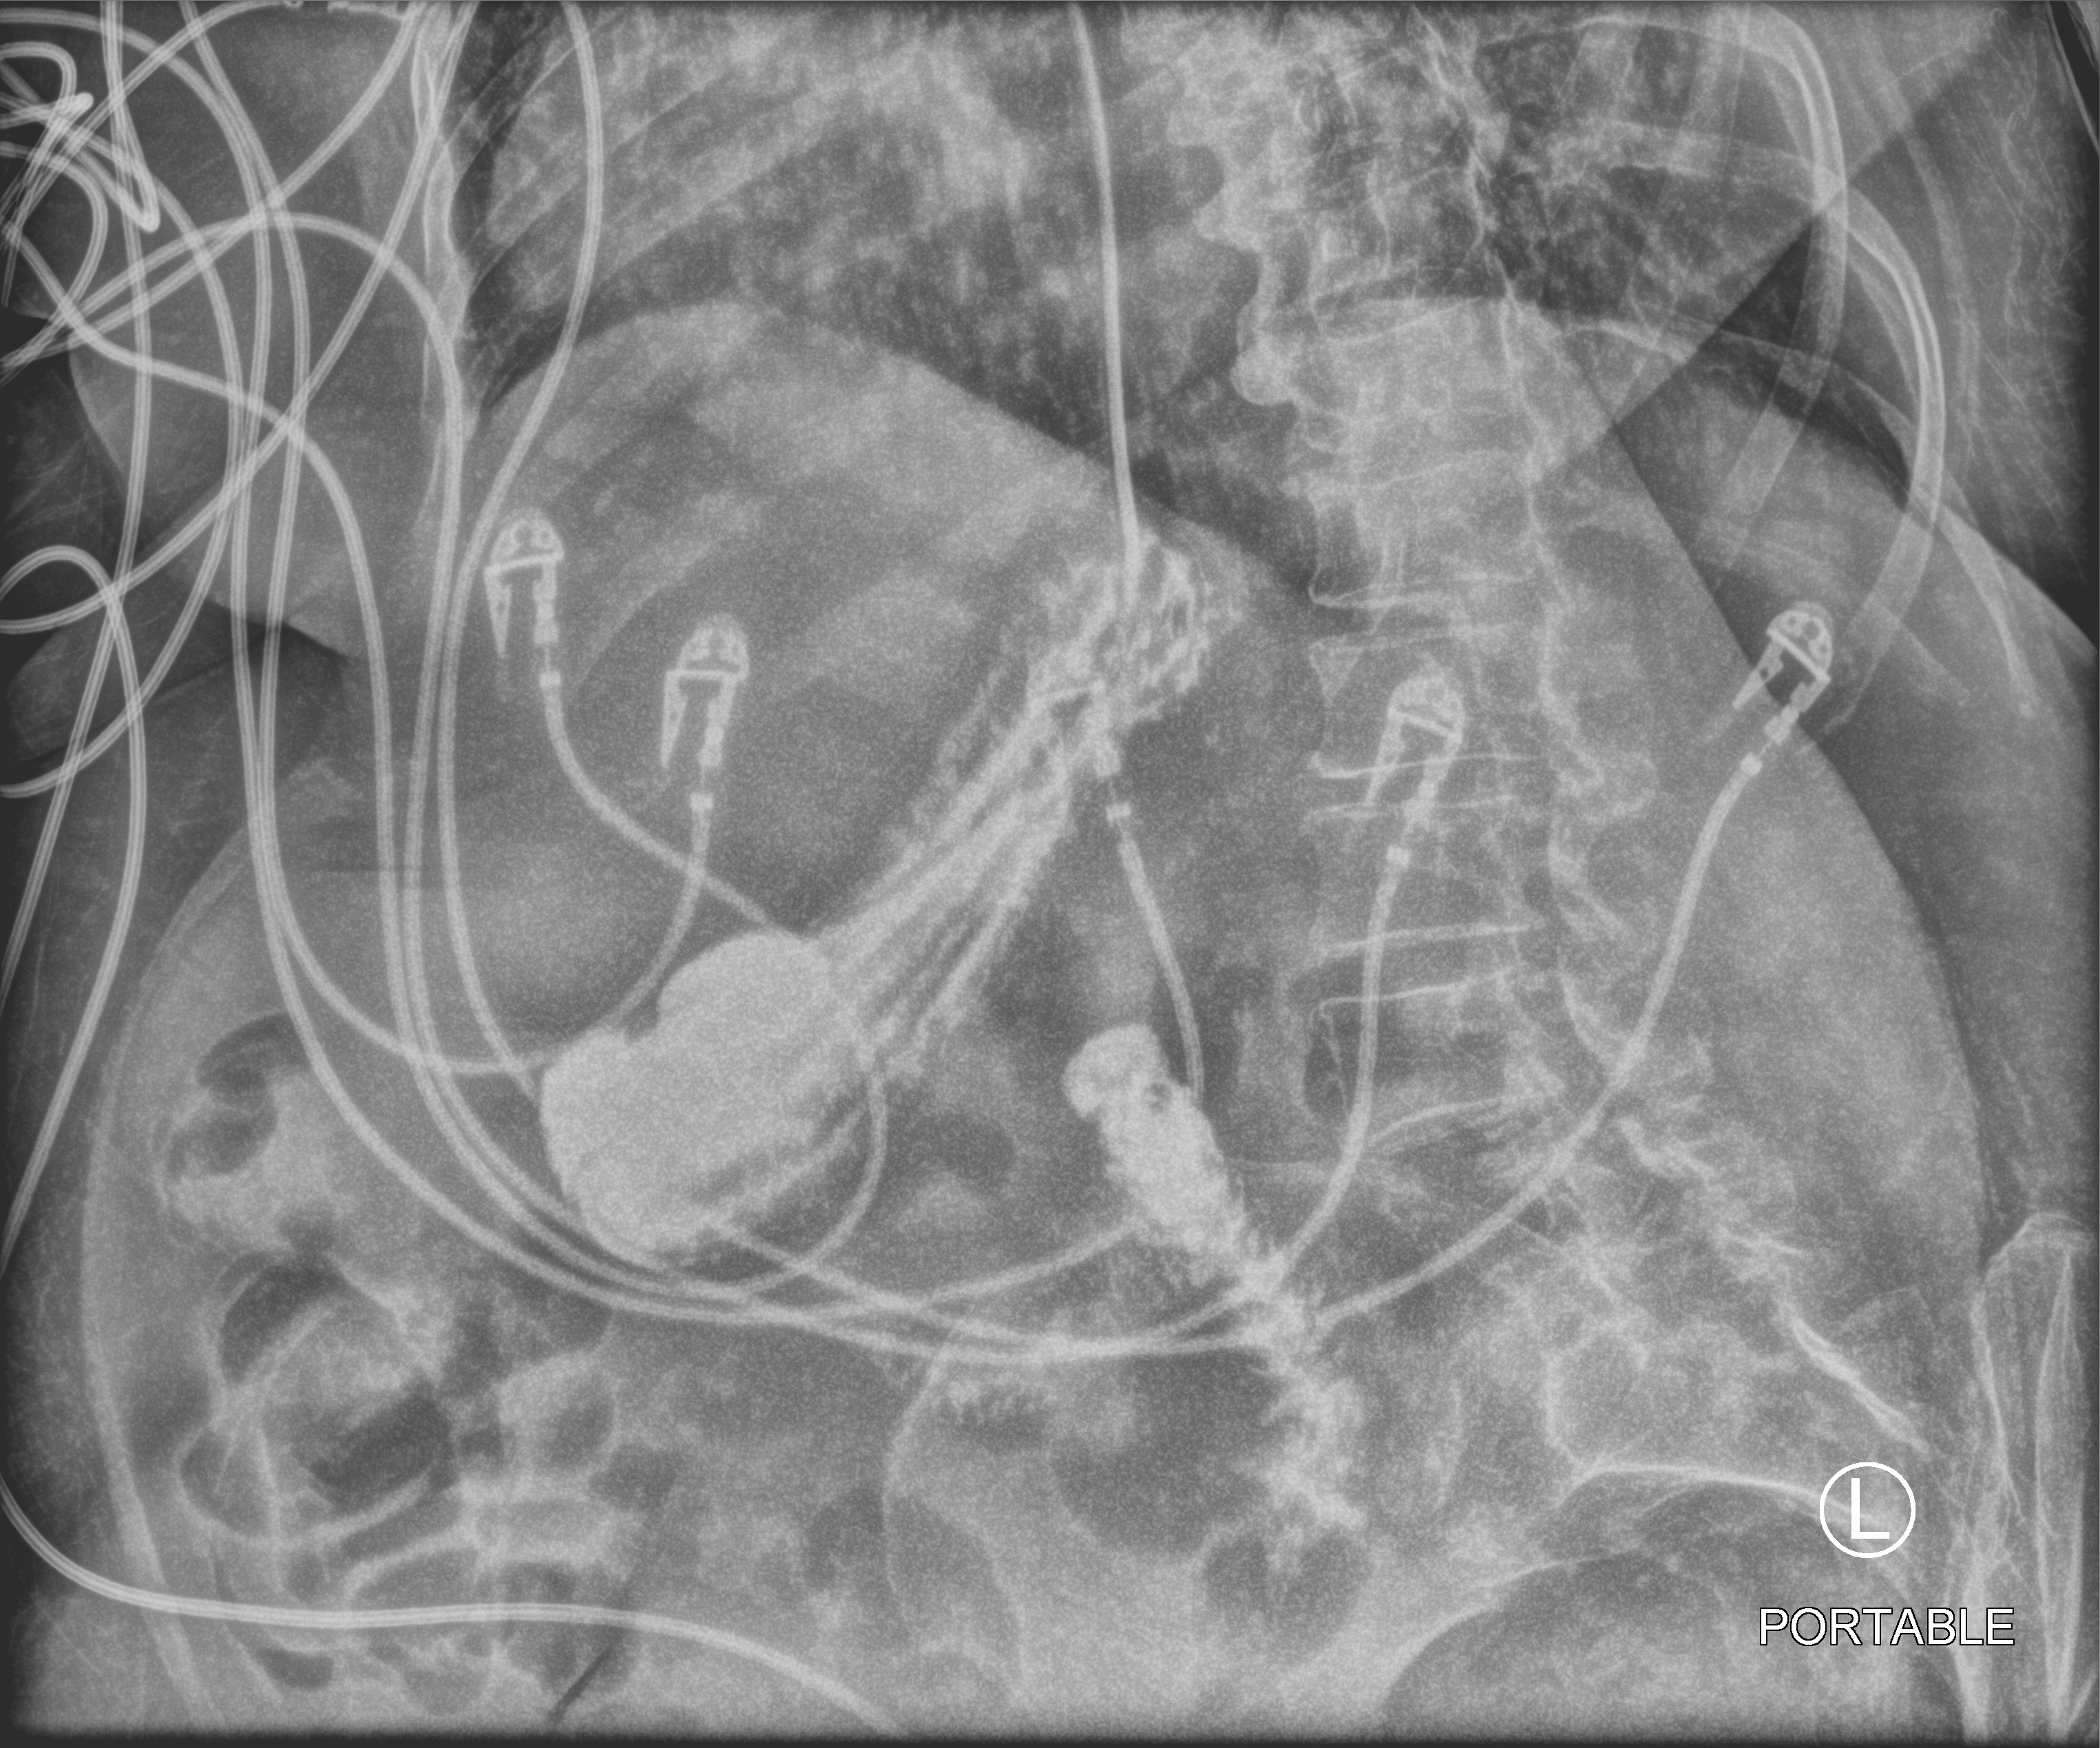
Portable abdomen radiograph; anteroposterior (AP) projection. Patient hospitalised with COVID-19; female, aged 75–90 years.
From the hospital-stay record, not from the radiograph (when in the stay this image was taken is not recorded): mechanically ventilated during this hospital stay: yes; admitted to intensive care during this hospital stay: yes; length of hospital stay: 31 days.